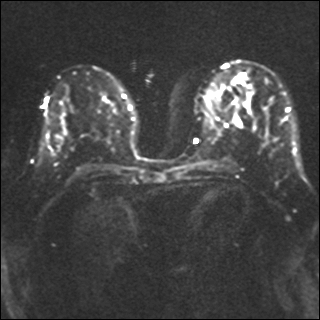
Breast MRI, one axial slice; position 17 of 40 along the scan axis; diffusion-weighted series; image 2 of 4 stored at this slice position (different b-values; order by instance number); 1.5 T; 4 mm slice thickness; 320 × 320 image matrix. Female patient.
Outlined on this slice (manually delineated by an expert):
- tumour on diffusion-weighted imaging: bounding box <232,114,242,128> (left, top, right, bottom; pixels)